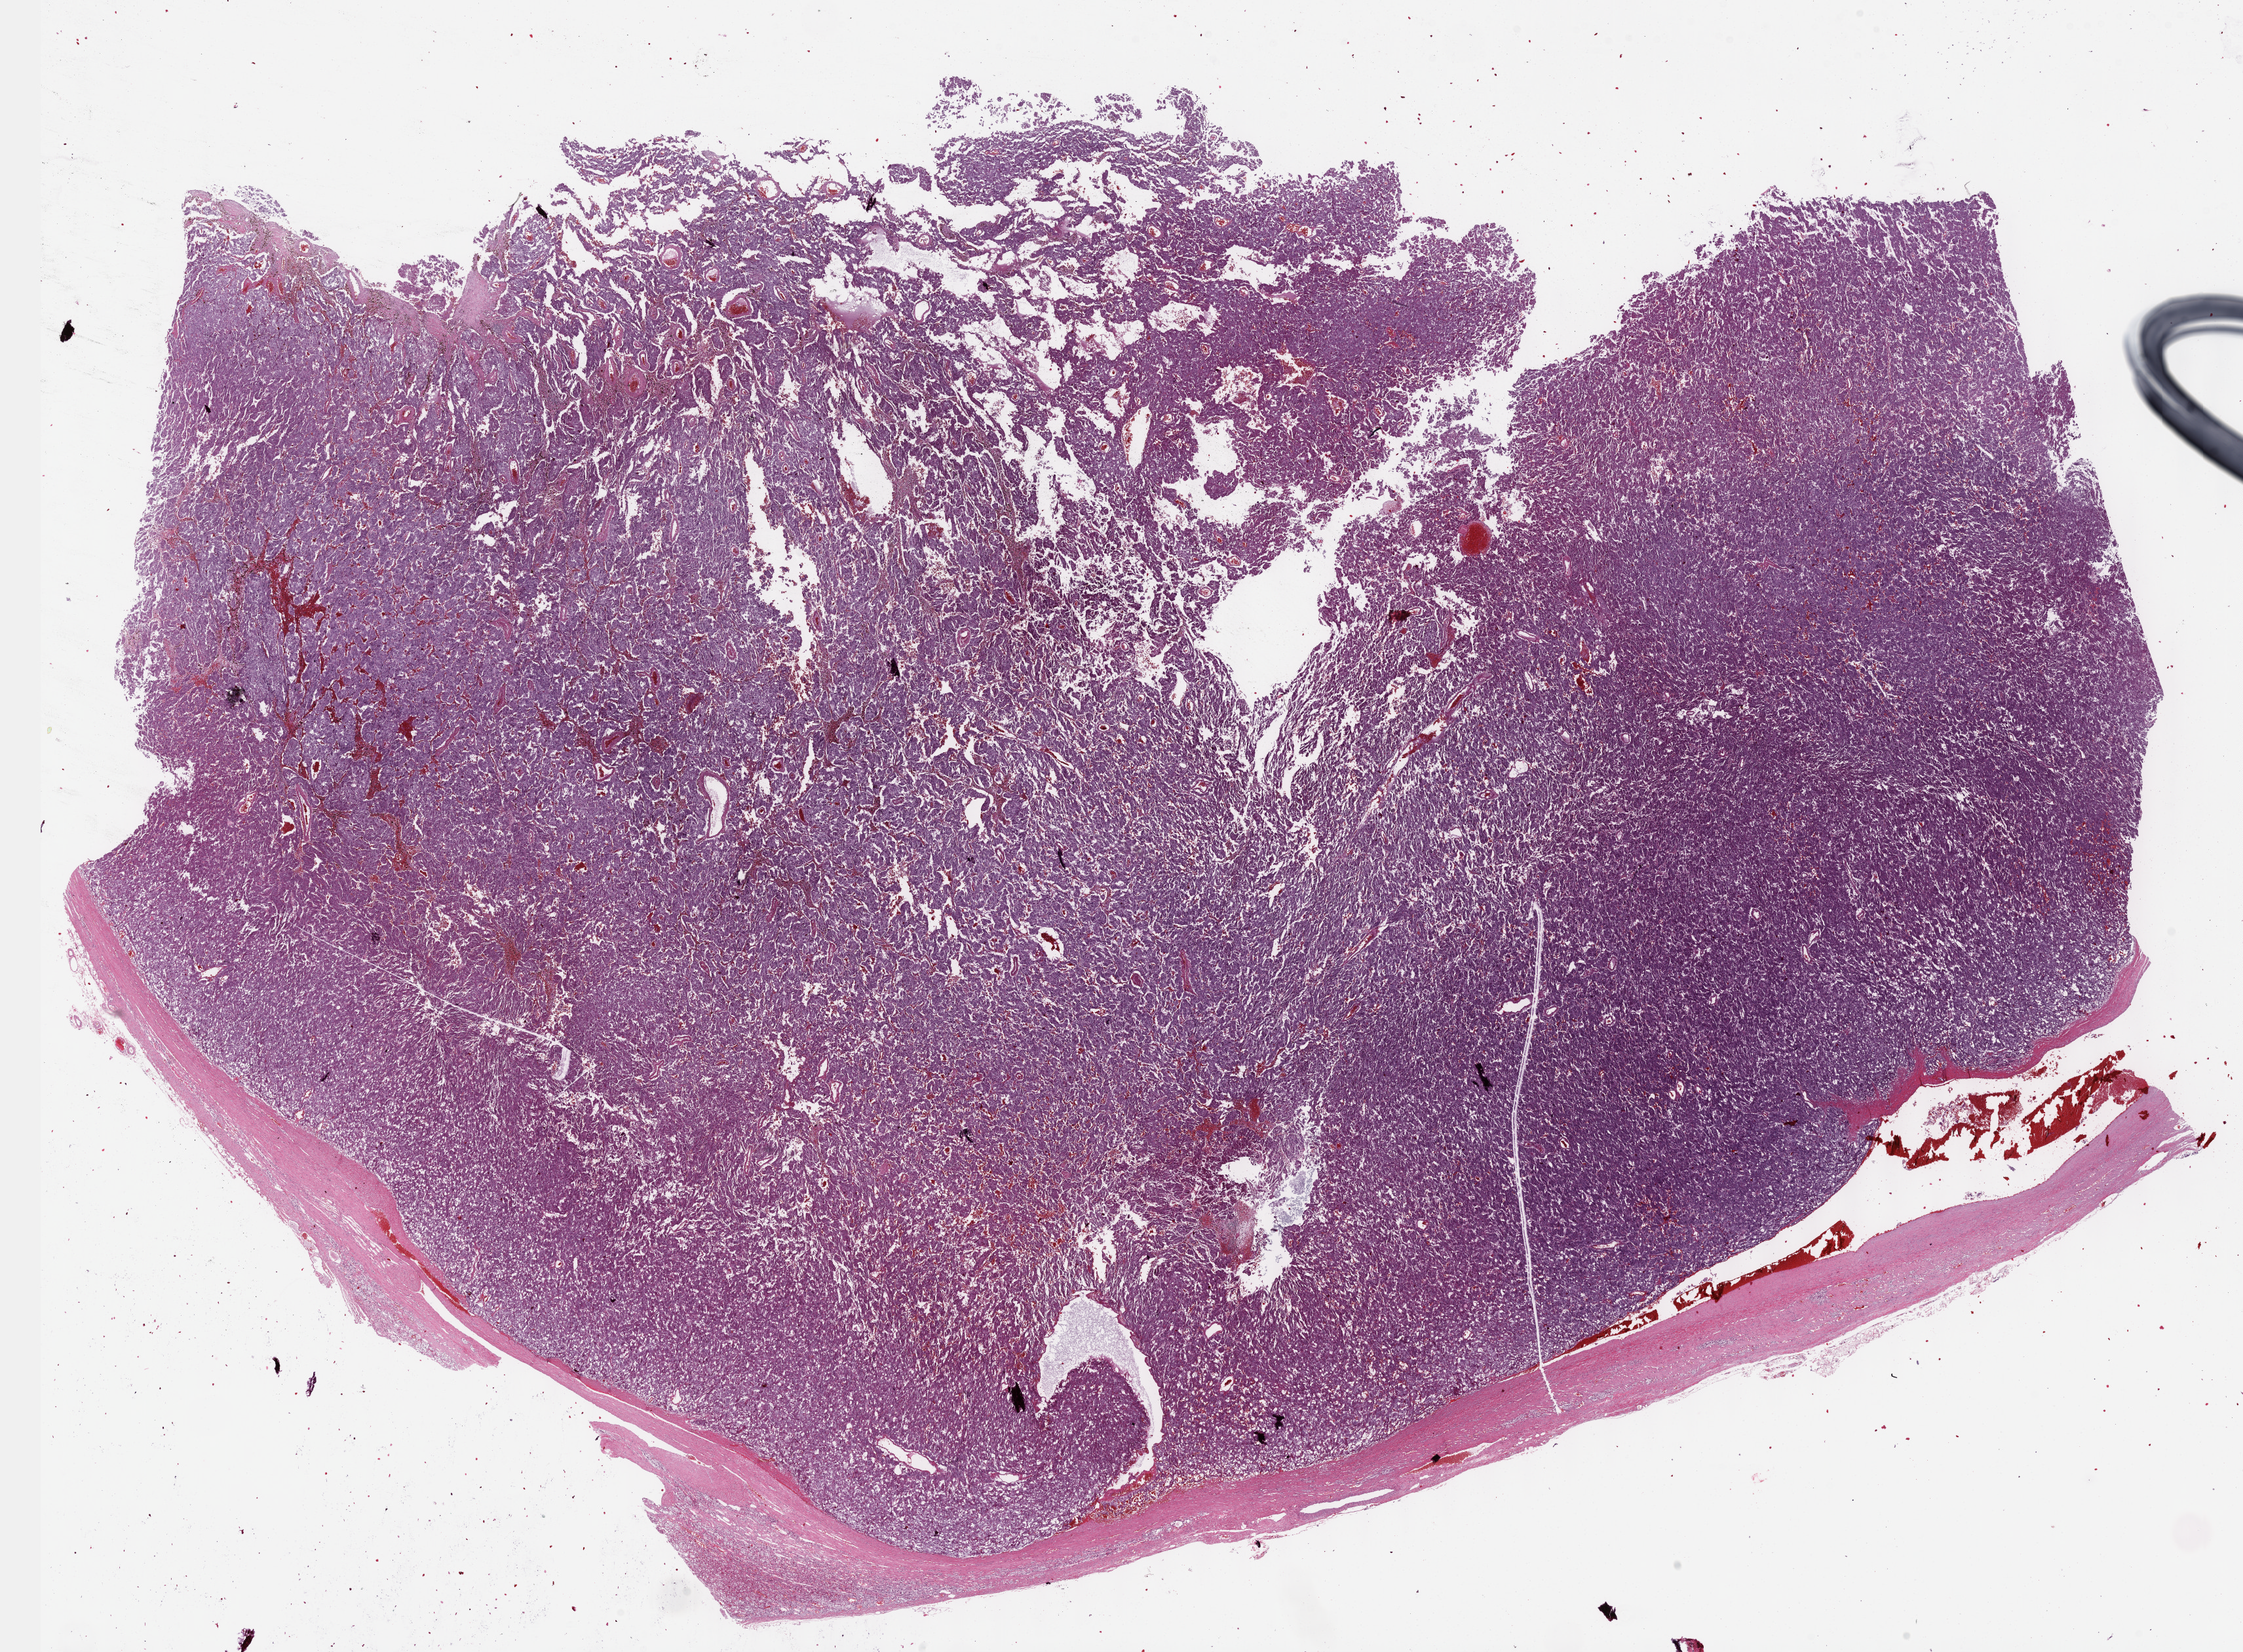
Whole-slide histology image, H&E-stained, whole scanned area (about 27.7 x 20.4 mm, acquisition: 40x scan) shown as a low-resolution overview; formalin-fixed paraffin-embedded (FFPE) diagnostic section; adrenal gland, primary tumour sample. Patient: female, age at initial diagnosis 63 years.
* pathologic diagnosis: Pheochromocytoma, NOS